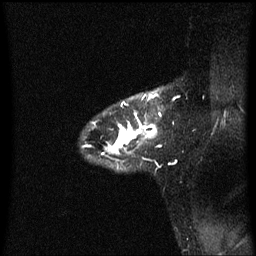
Breast MRI (dynamic contrast-enhanced), one sagittal slice. Position 47 of 60 along the scan axis. Dynamic contrast-enhanced series, image 2 of 3 at this slice position (ordered by acquisition). 1.5 T. TE 4.2 ms, TR 8.4 ms. 256 × 256 image matrix, field of view 200 × 200 mm. Female patient, age 32 years.
Annotated regions visible in this slice (semi-automatic segmentation, software-assisted and operator-edited):
- analysis volume of interest (the breast-tissue region the enhancement analysis was run in; not a lesion): bounding box (x1, y1, x2, y2) in pixels: (86, 90, 162, 167)
- tumour enhancement mask (voxels above the 70 % enhancement threshold inside the analysis volume of interest): (103, 94, 161, 155)